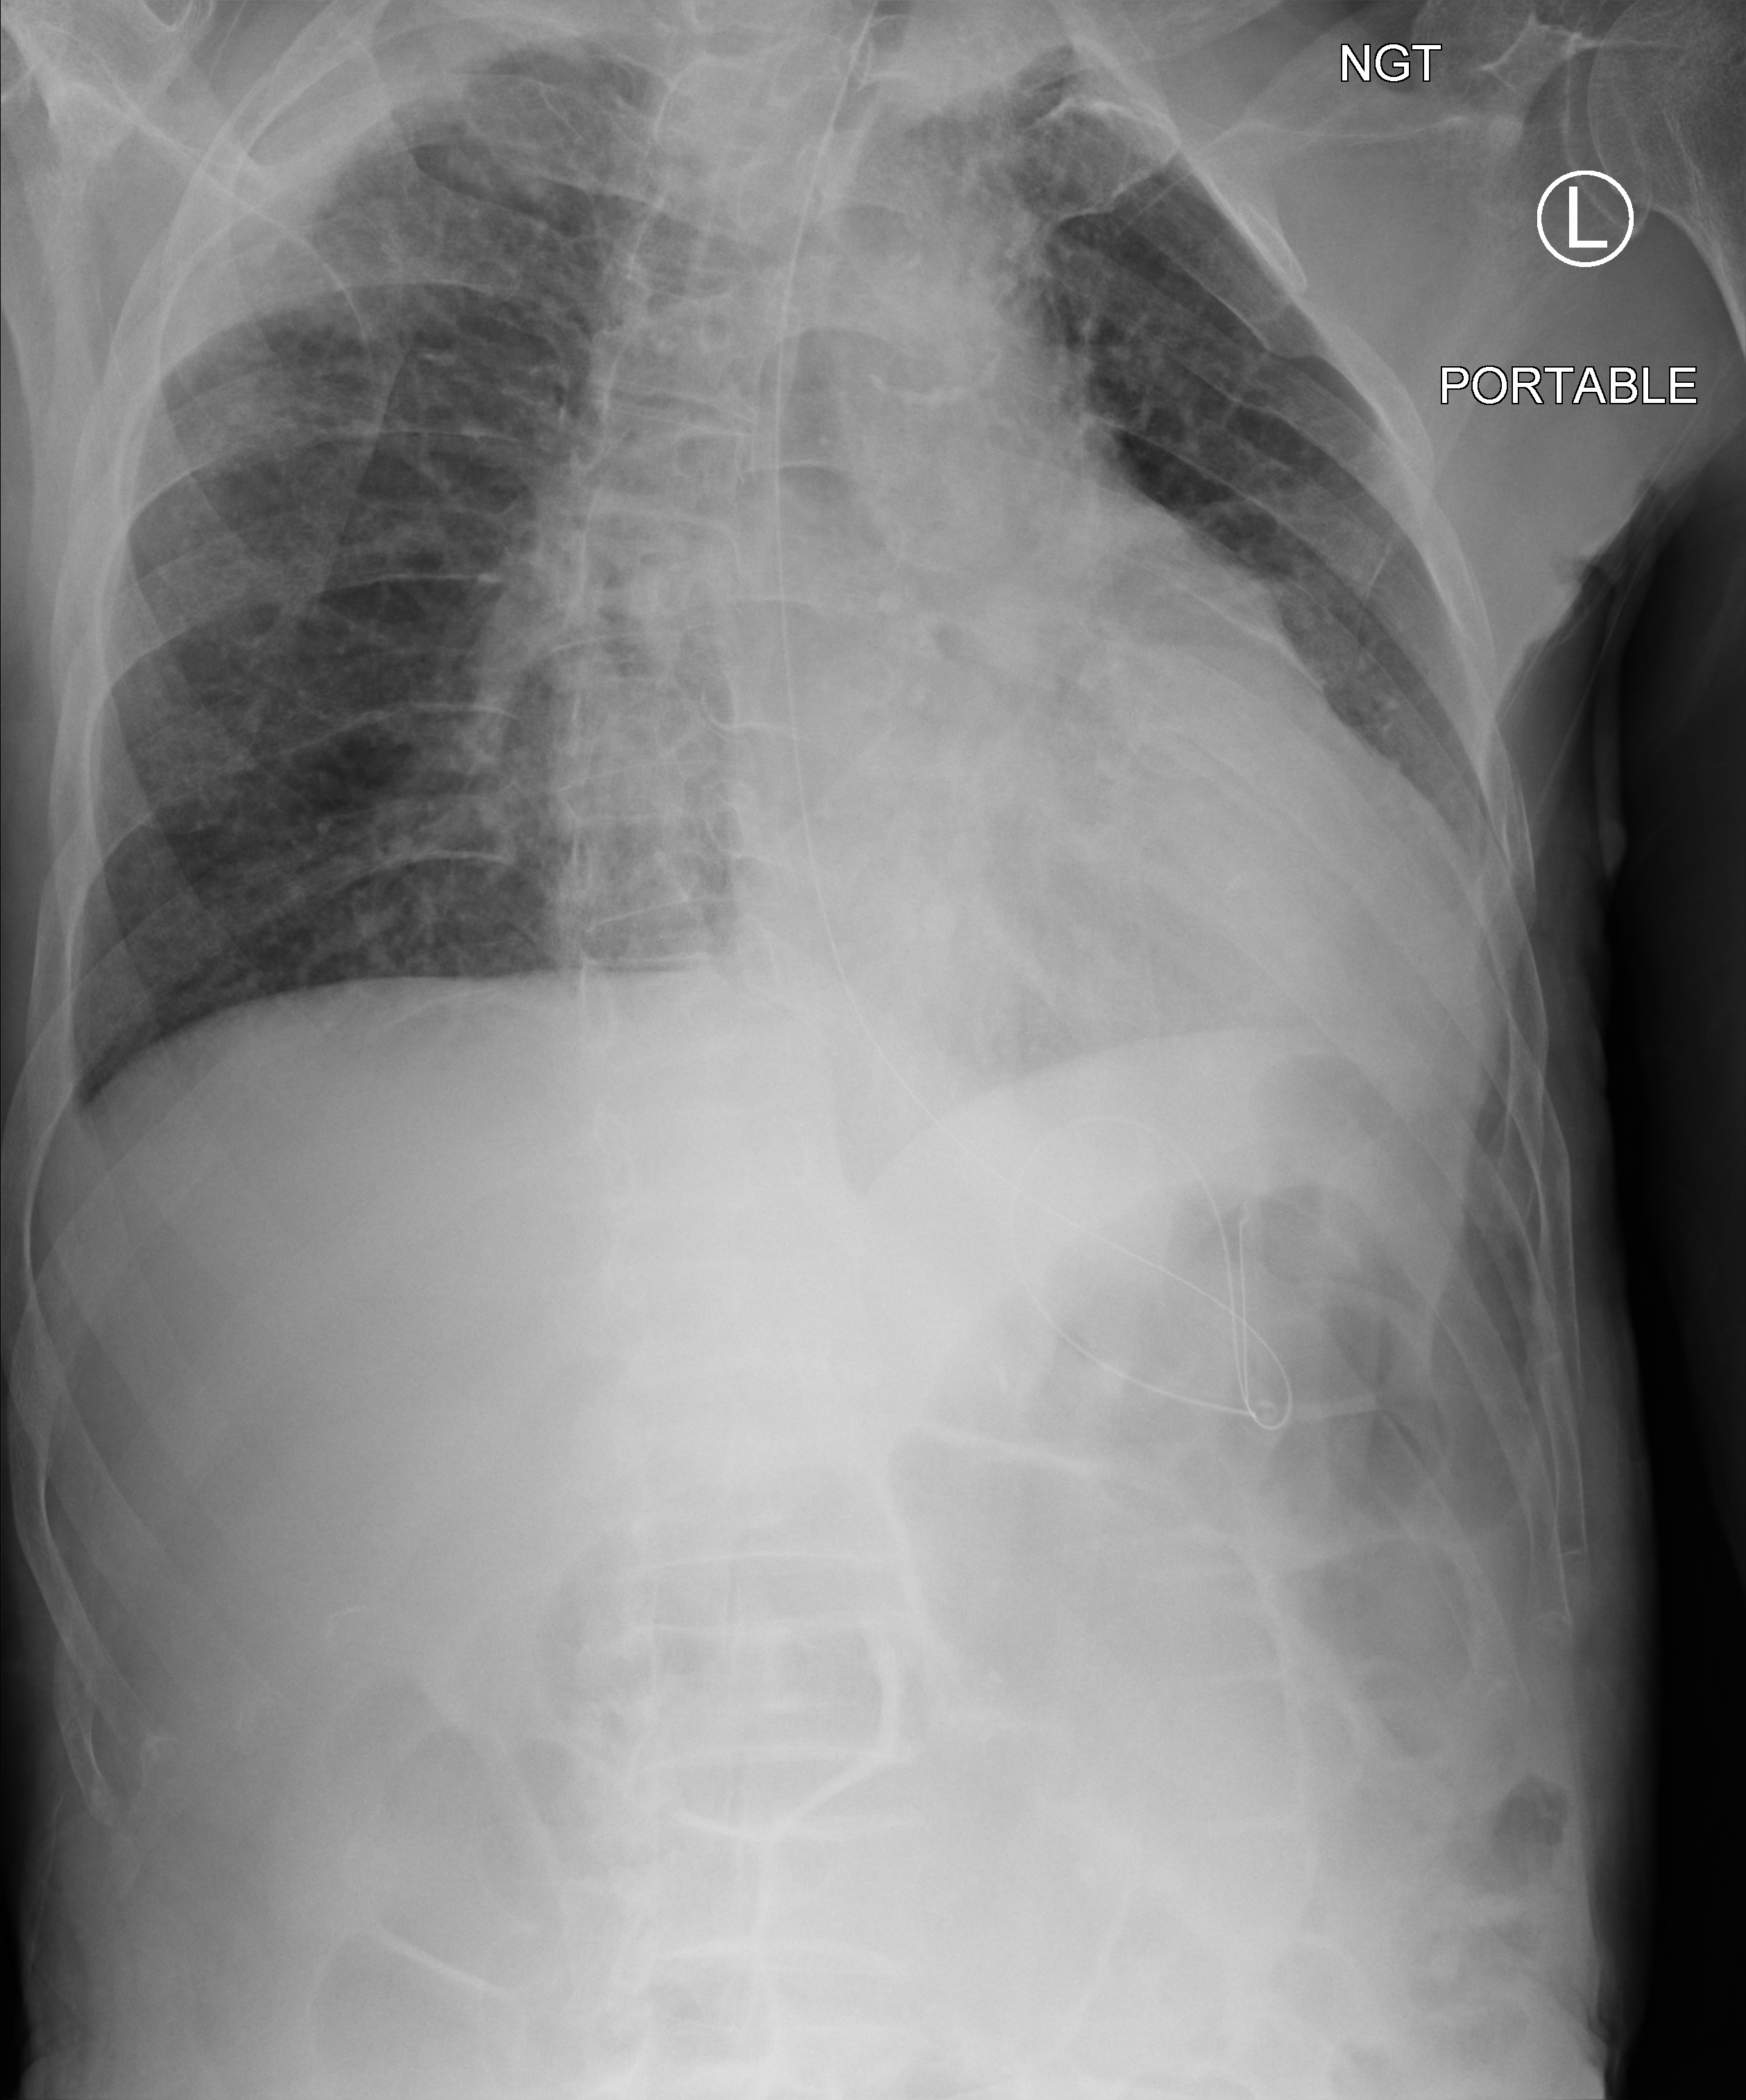
Bedside chest radiograph (computed radiography); anteroposterior (AP) projection. Patient hospitalised with COVID-19; male, aged 75–90 years.
Admission-level facts for this patient (not findings on this image; timing relative to this image not recorded): admitted to intensive care during this hospital stay: no; mechanically ventilated during this hospital stay: no; chronic kidney disease (admission record): no.